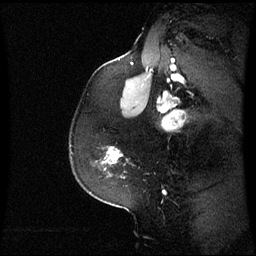
Breast MRI (dynamic contrast-enhanced), one sagittal slice. Position 46 of 60 along the scan axis. Dynamic contrast-enhanced series, image 2 of 3 at this slice position (ordered by acquisition). 1.5 T. TE 4.2 ms, TR 8.9 ms. 2.4 mm slice thickness. 256 × 256 image matrix, field of view 230 × 230 mm. Patient: female, 59 years. Case-level facts recorded for this patient, not image findings: setting: breast cancer imaged before/during neoadjuvant chemotherapy; receptor status: triple-negative.
Annotated regions visible in this slice (semi-automatically segmented with operator editing):
- analysis volume of interest (the breast-tissue region the enhancement analysis was run in; not a lesion): bounding box <103,147,128,164> (left, top, right, bottom; pixels)
- tumour enhancement mask (voxels above the 70 % enhancement threshold inside the analysis volume of interest): <105,147,119,164>